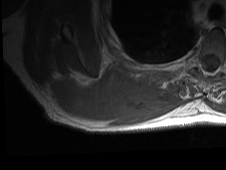
MRI of an extremity soft-tissue mass, one axial slice. Position 25 of 81 along the scan axis. MR volume resampled by the dataset authors to the PET/CT grid (not the native acquisition matrix). 3.27 mm slice thickness. 226 × 170 image matrix. Male patient. From the clinical record (not read from this slice): histological type: pleiomorphic spindle cell undifferentiated; grade: high; site of the primary tumour: right parascapusular.
Outlined on this slice (expert contour drawn on MRI and transferred to this co-registered scan by the dataset authors):
- gross tumour volume including surrounding oedema: box from (x=46, y=67) to (x=182, y=126) px
- gross tumour volume (mass): (x=53, y=70)–(x=148, y=121)